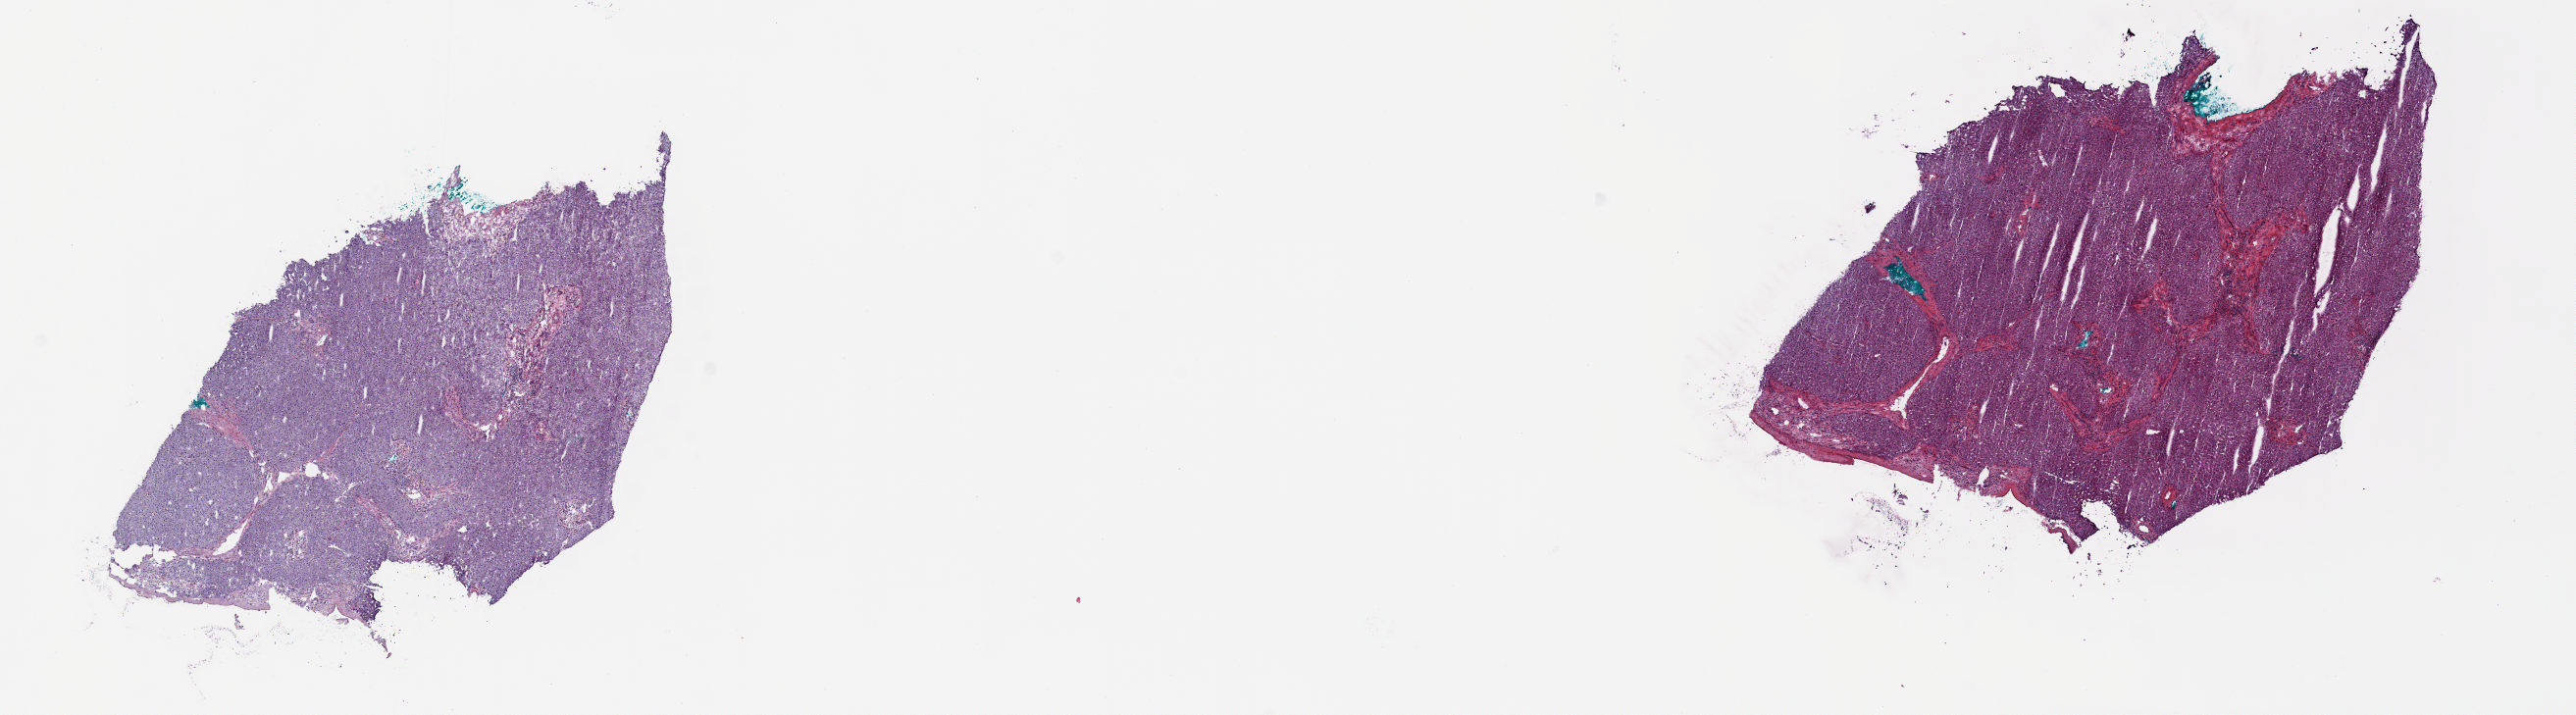
H&E-stained whole-slide image, whole scanned area (about 20.8 x 5.8 mm) shown as a low-resolution overview, frozen section from the top of the tissue portion, liver, solid tissue normal (non-tumour tissue) sample. Patient: female, age at initial diagnosis 84 years. Pathologist review of this section (percent, as recorded): tumour cells 0%, tumour nuclei 0%, normal cells 75%, stromal cells 25%, necrosis 0%. Inflammatory infiltration, as recorded: lymphocyte infiltration 5%, monocyte infiltration 2%, neutrophil infiltration 0%.
This section: solid tissue normal (non-tumour) sample from the same patient. Patient diagnosis: Hepatocellular carcinoma, NOS.